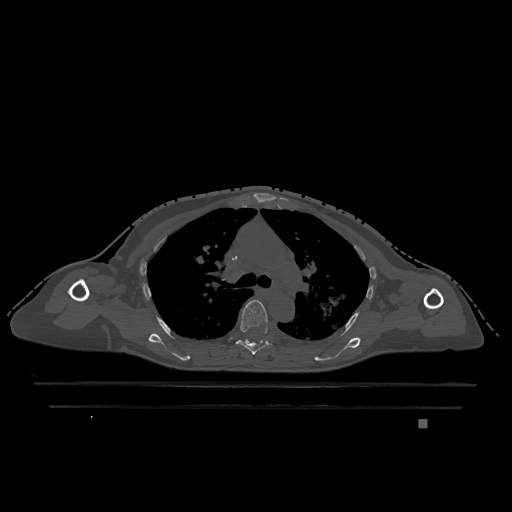
CT including the spine, one axial slice. Slice 834 of 1317 in the series (ordered by position). Bone window (W 1800 / L 400 HU). 512 × 512 image matrix. Patient: female, 74 years. Case-level facts recorded for this patient, not image findings: primary cancer: lung; vertebrae with lytic lesions (as recorded): T1, T4, T5, T6, L4, L5.
Outlined on this slice (semi-automatically segmented with operator editing):
- T5 vertebra: bounding box [x1, y1, x2, y2] px = [236, 300, 272, 355]